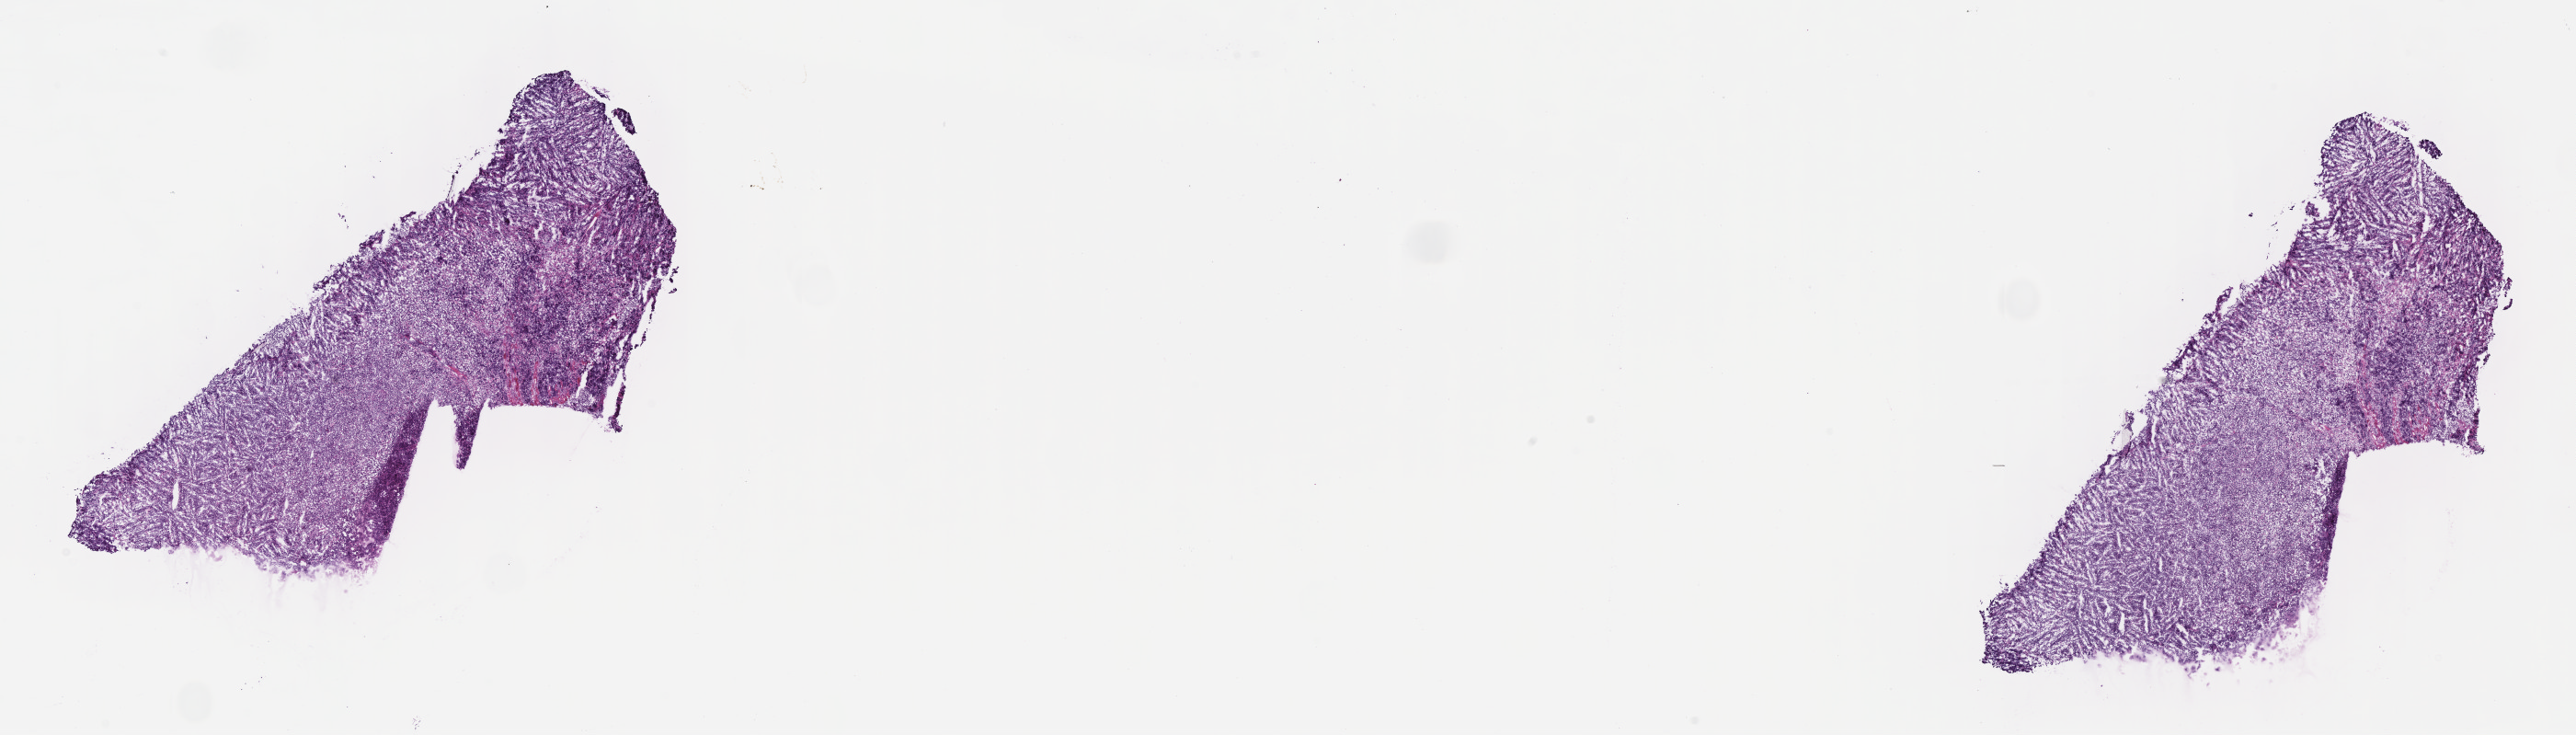
Whole-slide image, H&E stain, whole scanned area (about 22.6 x 6.5 mm) shown as a low-resolution overview, frozen section (tissue freezing medium), primary tumor, anatomic site: cranium. Male patient; age at initial diagnosis 9 years. Slide review estimates, as recorded: tumor cells 90%, tumor nuclei 90%, stromal cells 10%, necrosis 0%, normal cells 0%. Inflammatory infiltration, as recorded: lymphocyte infiltration 30%, monocyte infiltration 30%, neutrophil infiltration 20%.
Diagnosis: Burkitt lymphoma, NOS. Ann Arbor stage (patient): Stage IV.